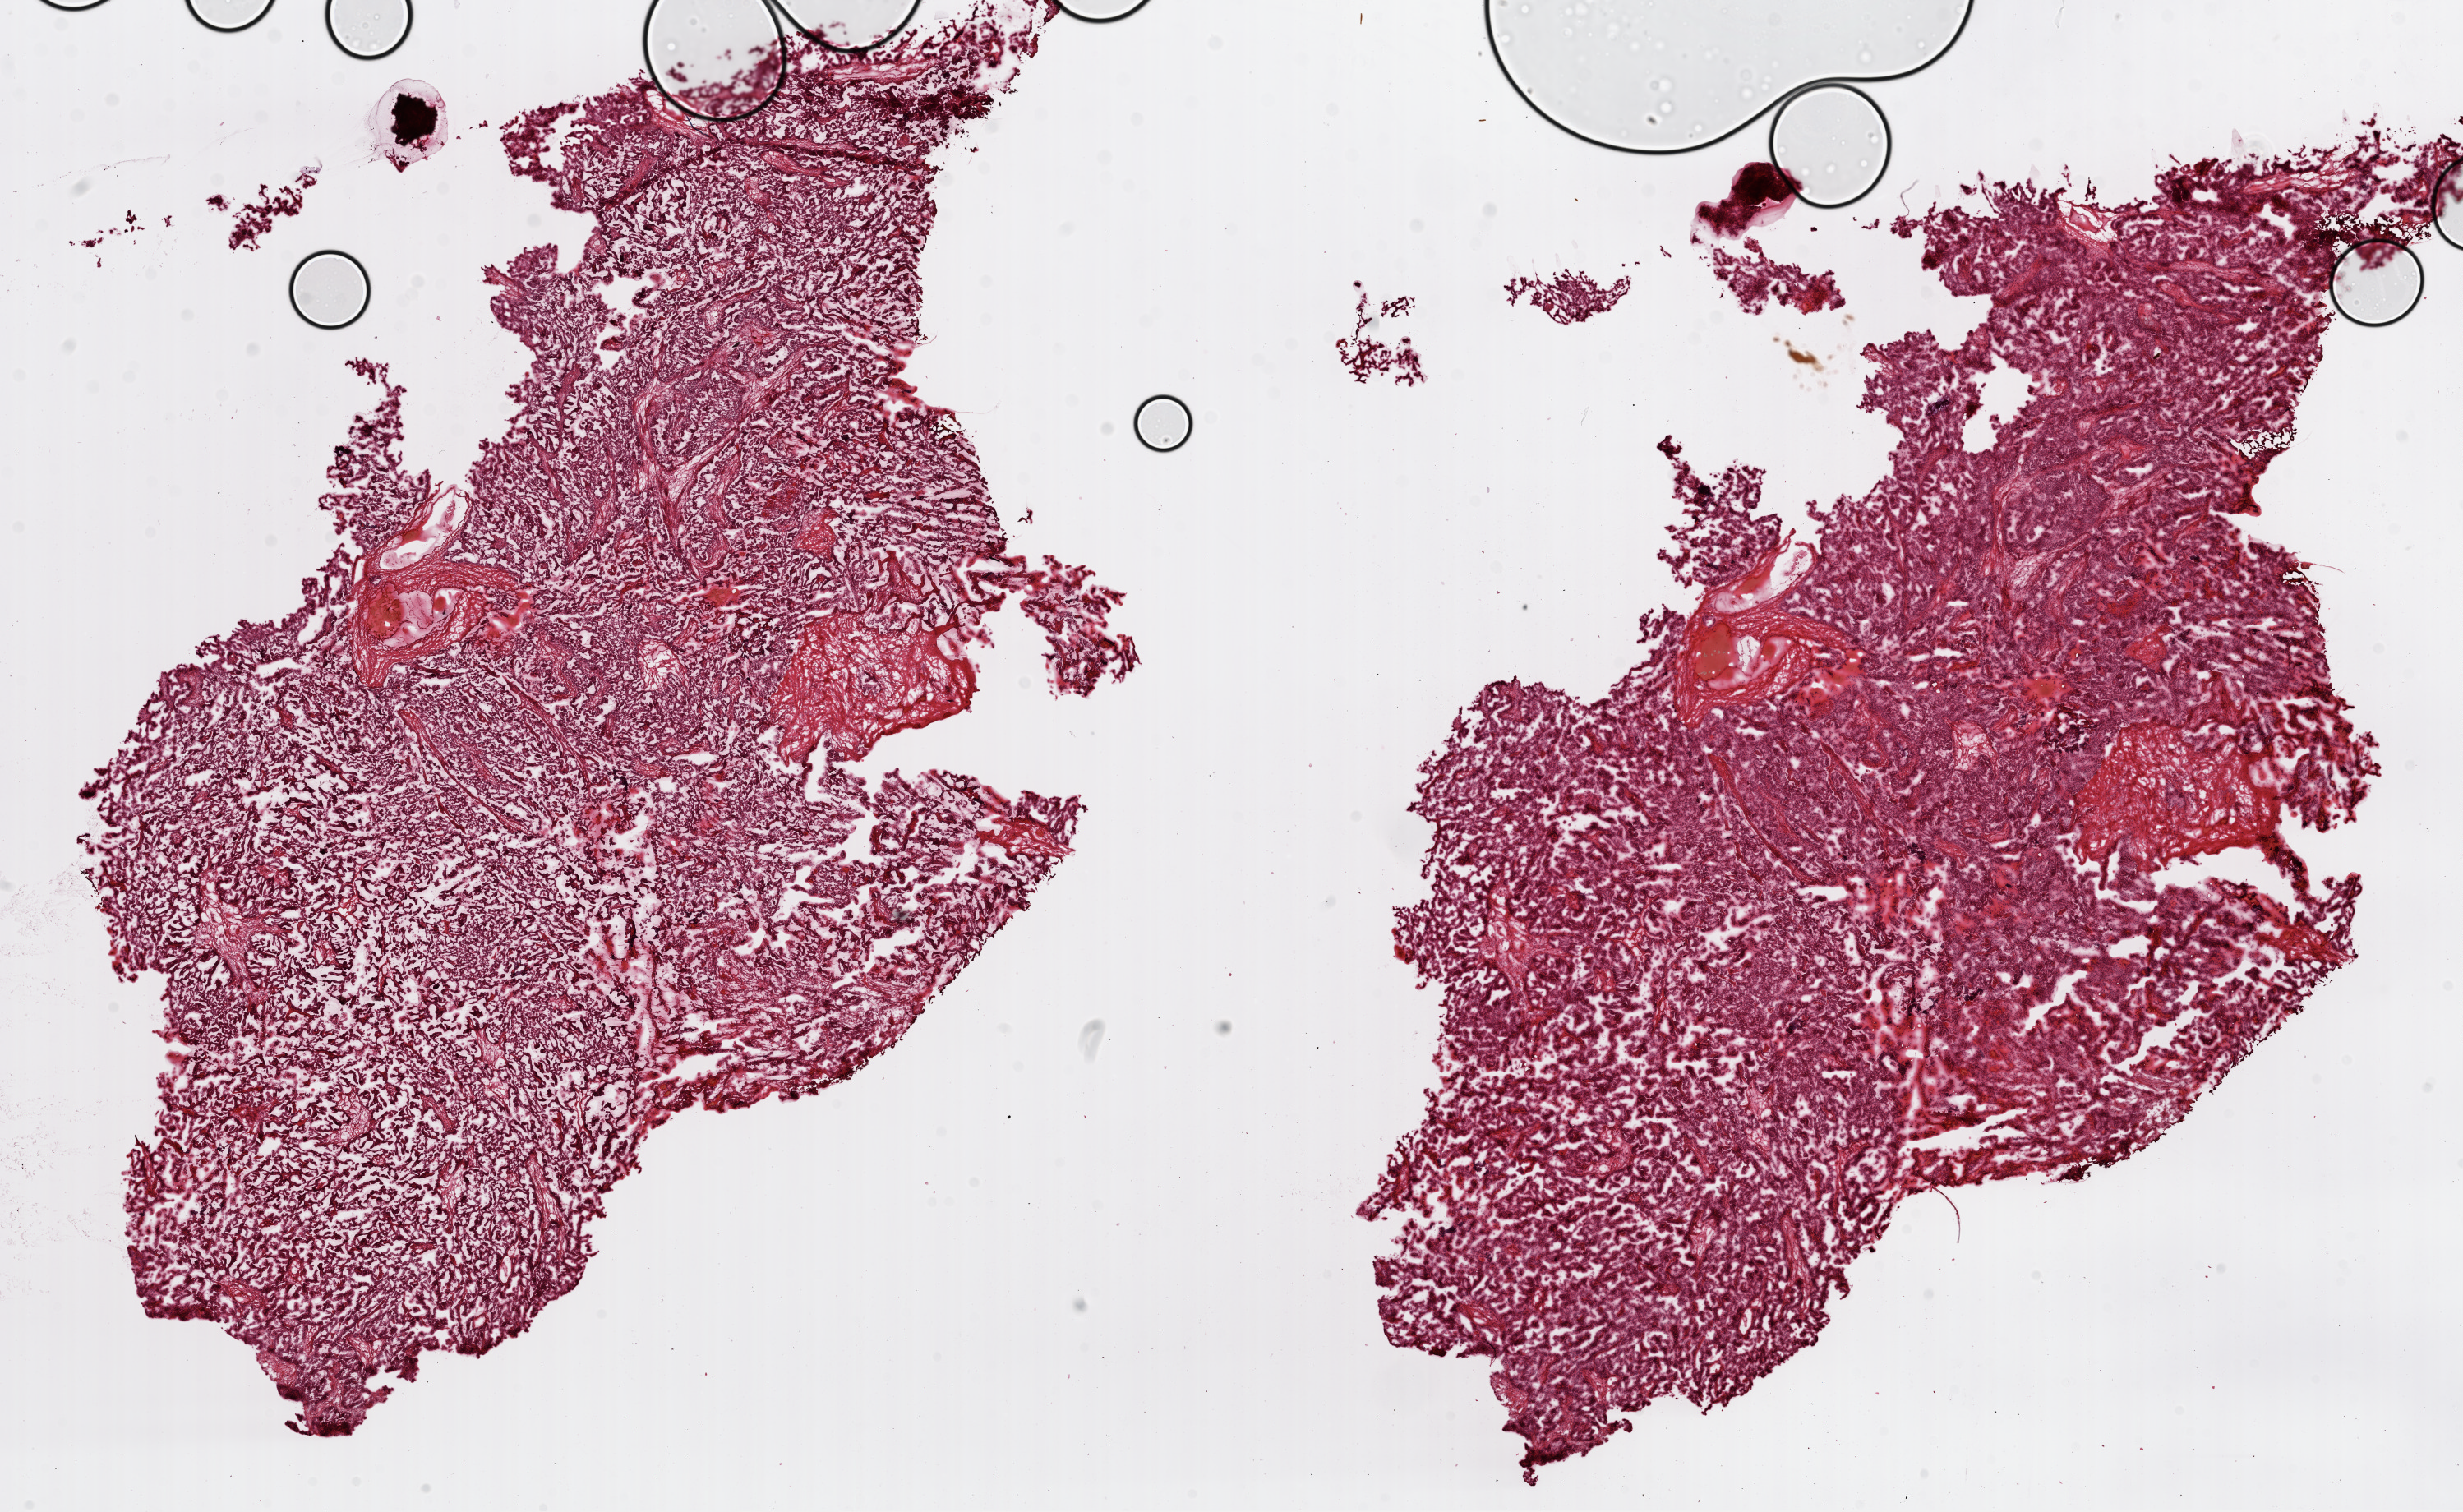
Digitized H&E-stained tissue section (whole slide) — whole scanned area (about 24.2 x 14.8 mm) shown as a low-resolution overview, frozen section from the top of the tissue portion, ovary, primary tumour sample. Female, age 50 years at initial diagnosis. Histologic grade: G3 (poorly differentiated). Composition of this section per pathologist review: tumour cells 0%, tumour nuclei 90%, normal cells 0%, stromal cells 0%, necrosis 5%.
- pathologic diagnosis: Serous cystadenocarcinoma, NOS
- FIGO stage: IIIC
- laterality: bilateral